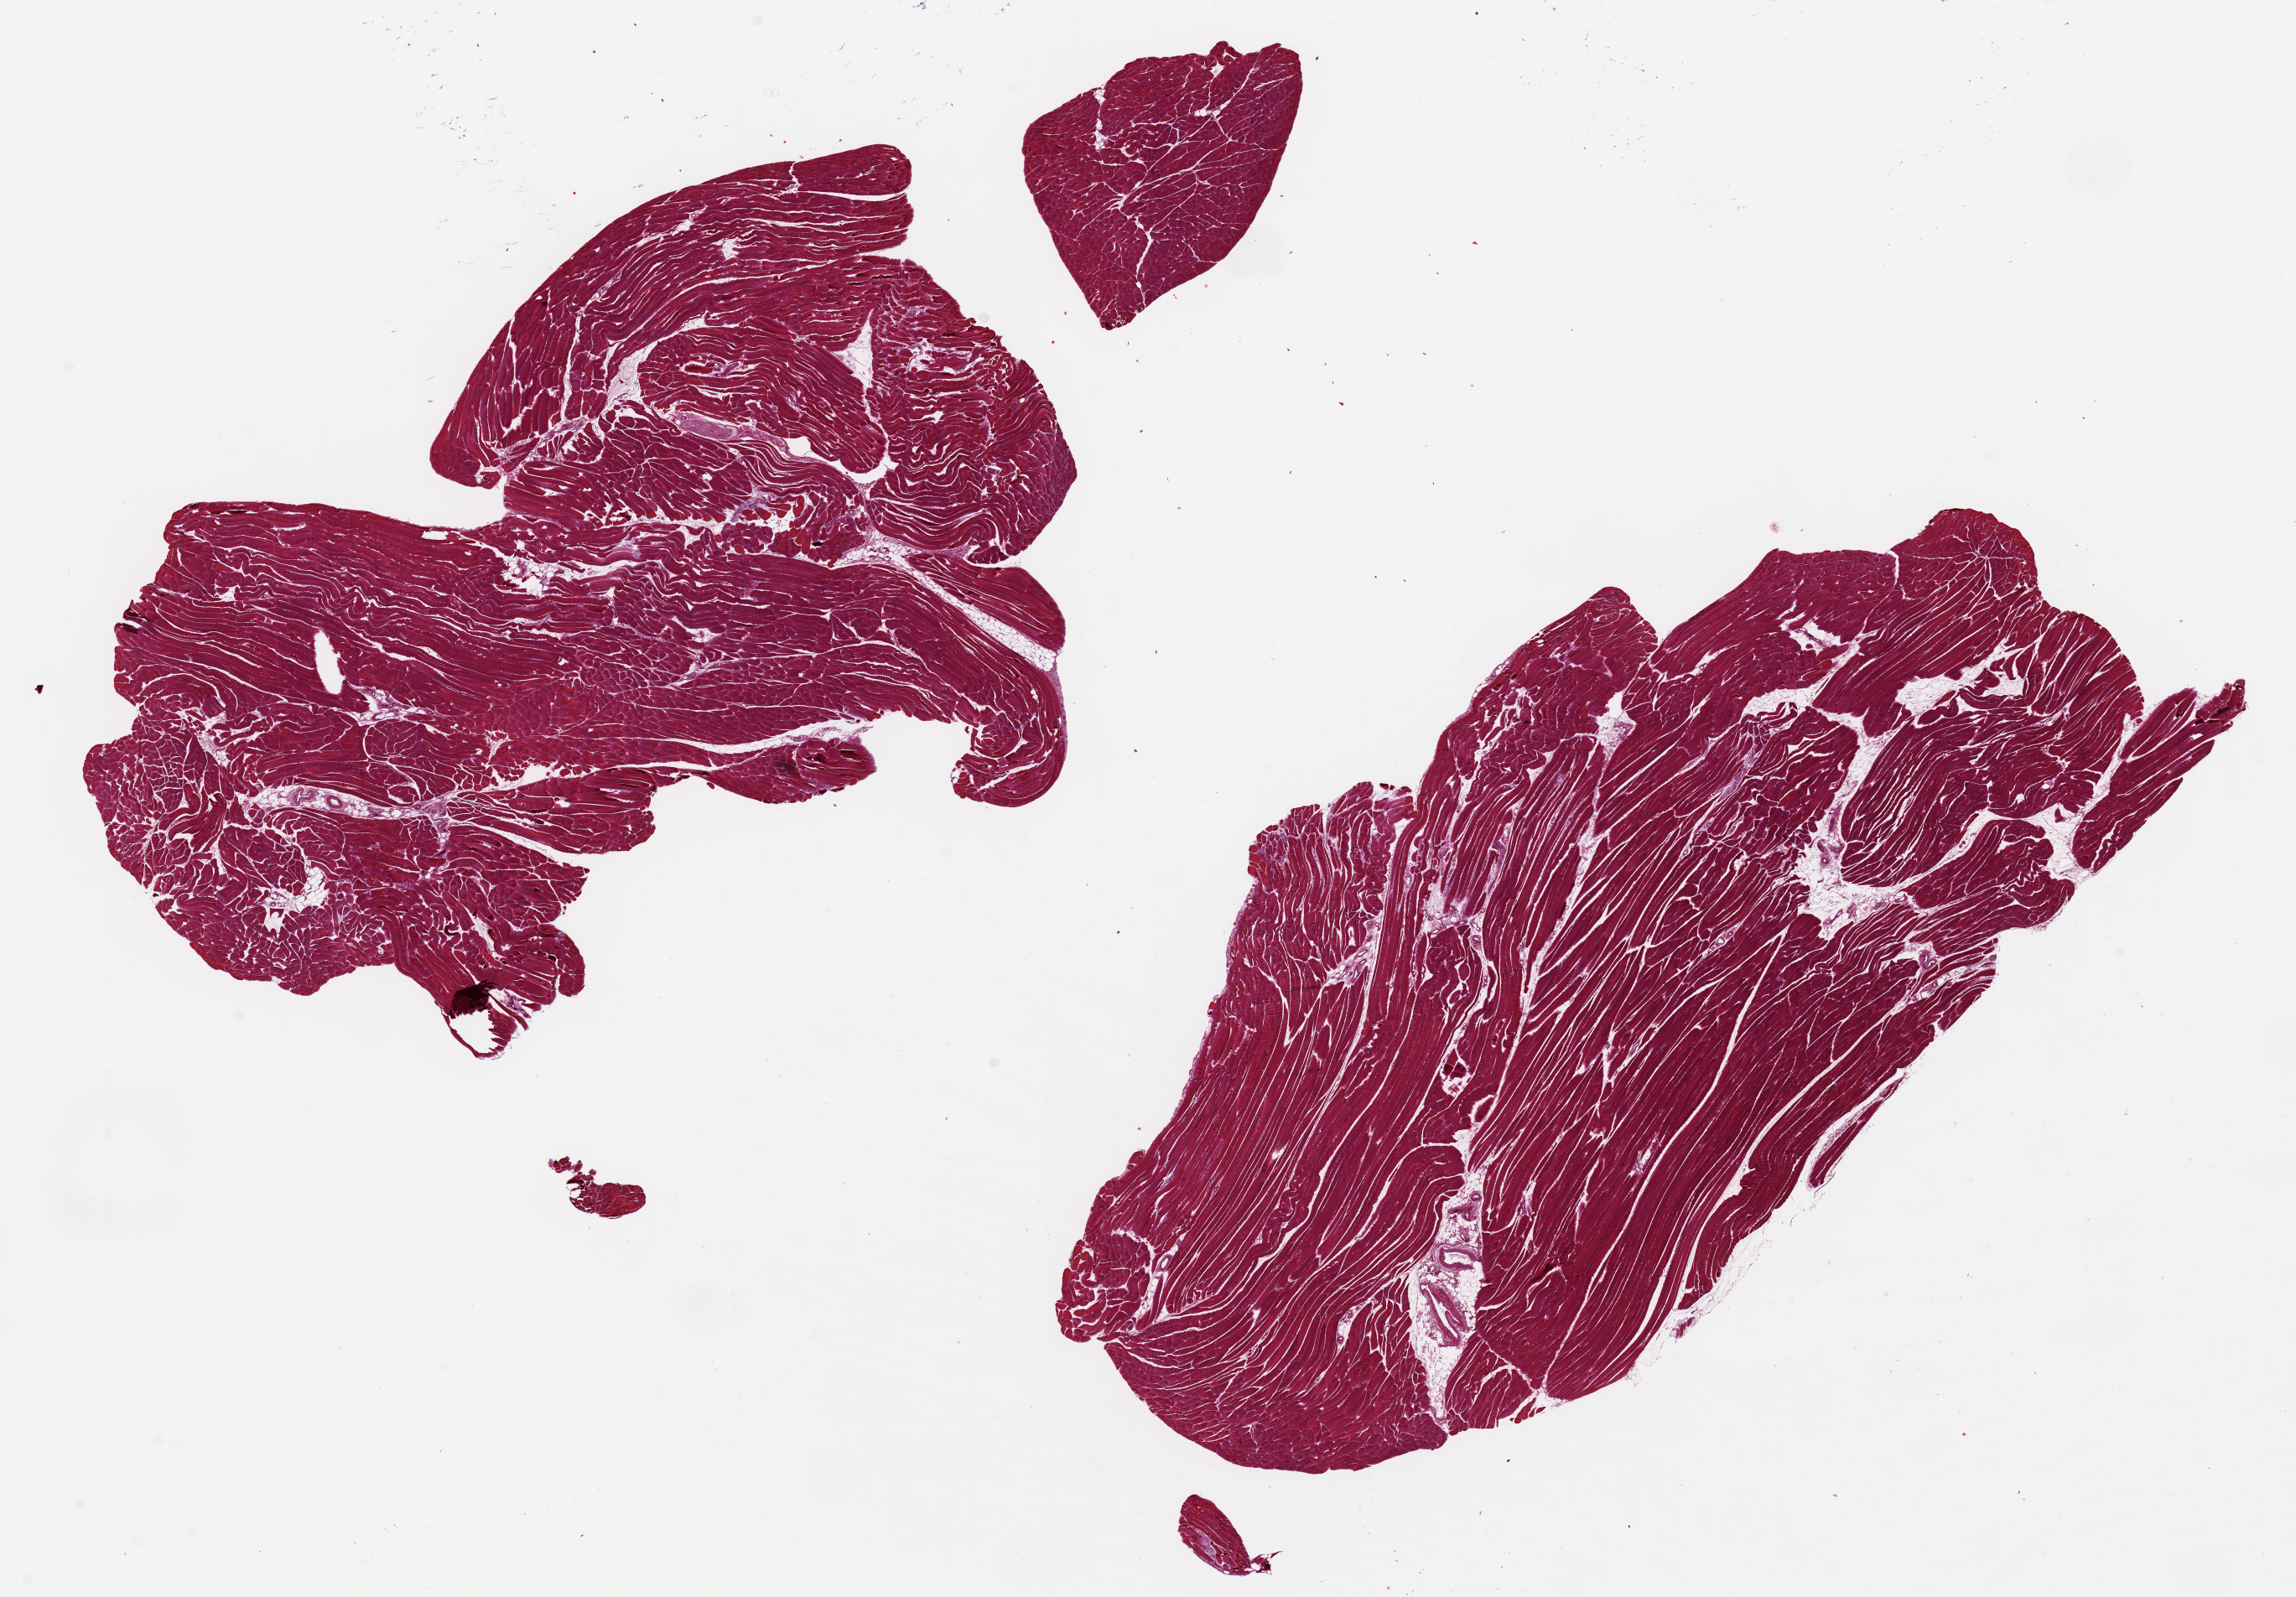
Digitized haematoxylin and eosin-stained section — a low-resolution overview of the entire scanned area, about 21.7 x 15.1 mm (acquisition: 20x scan). PAXgene-fixed, paraffin-embedded tissue. Target tissue: skeletal muscle. Tissue donor sample. Donor: female.
- reviewer comment on this tissue sample: 2 pieces up to ~11x6mm